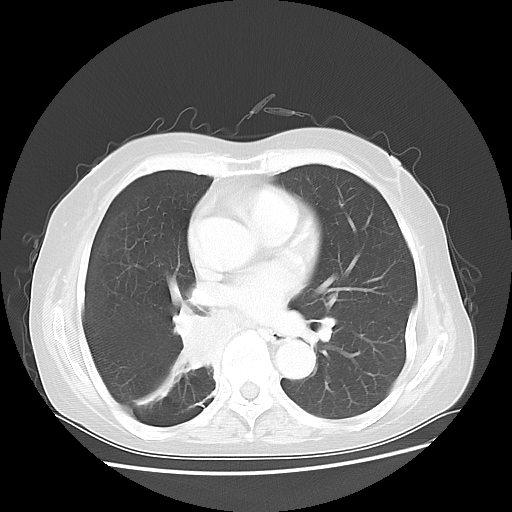
Chest CT, one axial slice; position 23 of 47 along the scan axis; reconstruction kernel LUNG; lung window (W 1500 / L -600 HU); 5 mm slice thickness; 512 × 512 image matrix, field of view 360 × 360 mm. Patient: female, 63 years. From the clinical record (not read from this slice): clinical TNM (as recorded): T2 N3 M1b; histopathological grade: G3.
Outlined on this slice (rectangle marked by the reading radiologist):
- lung tumour (recorded histology: small cell carcinoma): bounding box [x1, y1, x2, y2] px = [160, 303, 221, 393]